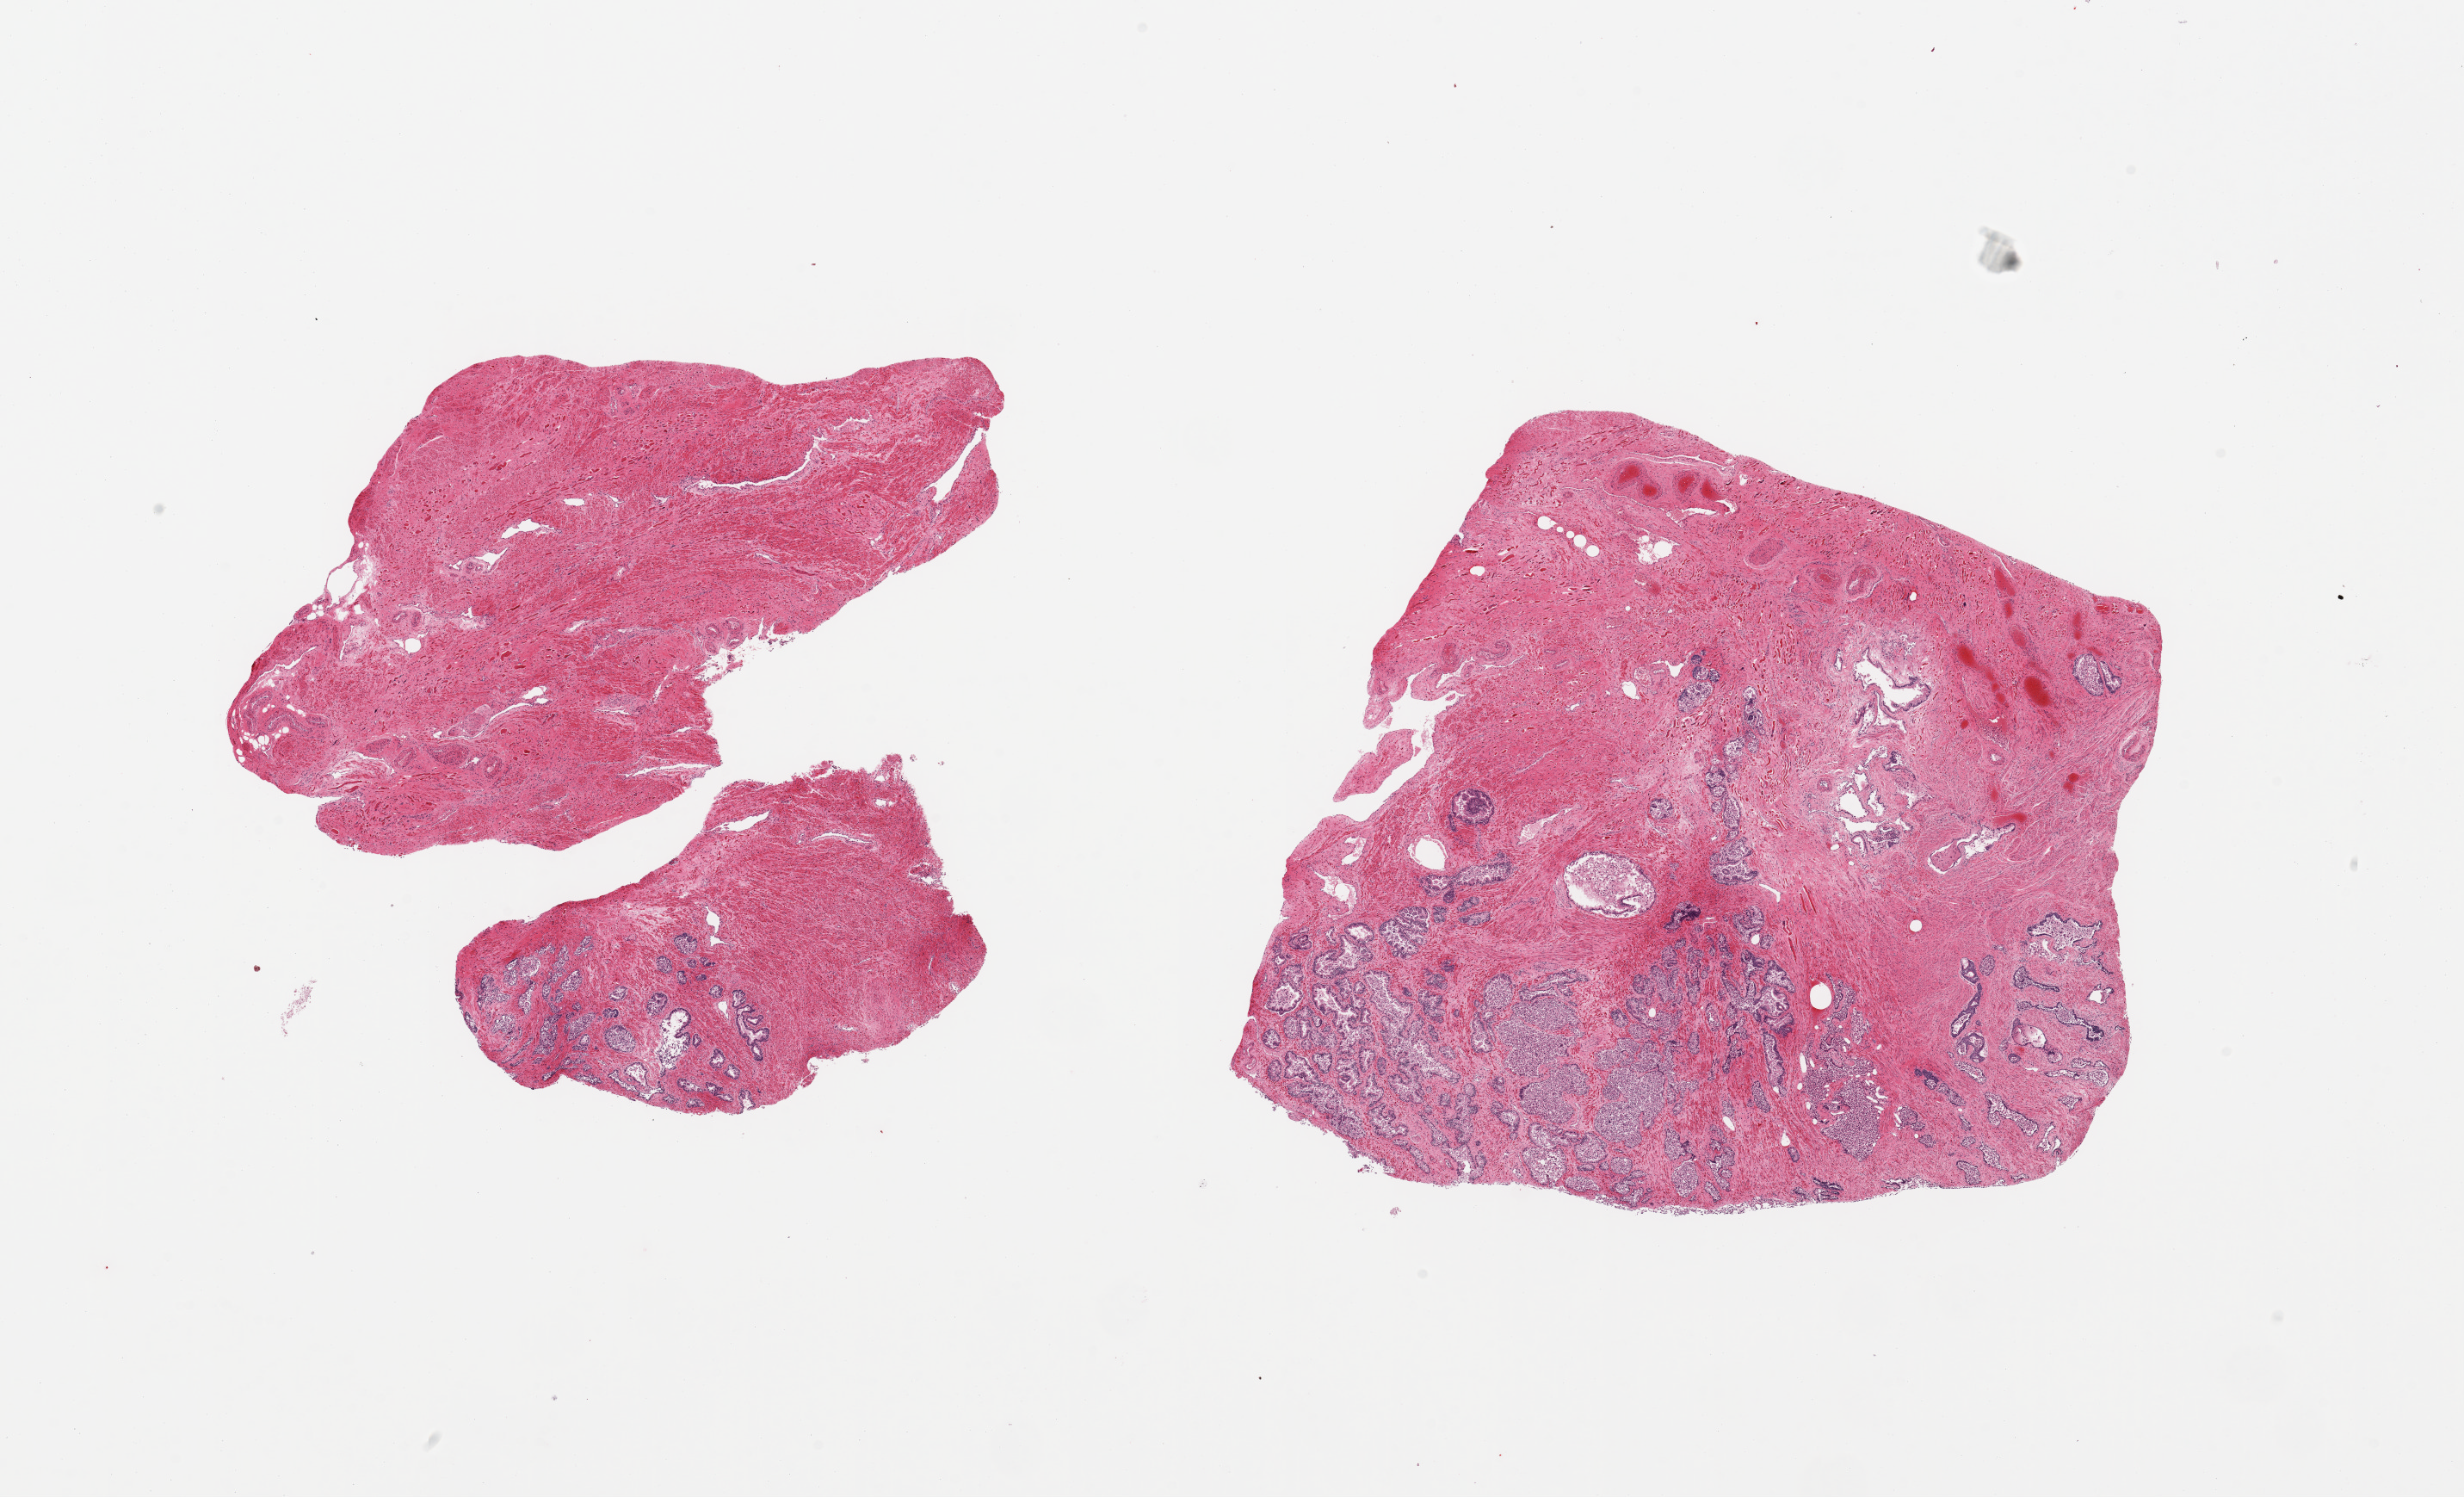
H&E whole-slide image, whole scanned area (about 22.6 x 13.8 mm) shown as a low-resolution overview. PAXgene-fixed, paraffin-embedded tissue. Sampled site (target tissue): prostate. Tissue donor sample. Donor sex: male.
Reviewer comment on this tissue sample: 2 pieces; glands largely autolyzed, stroma intact.